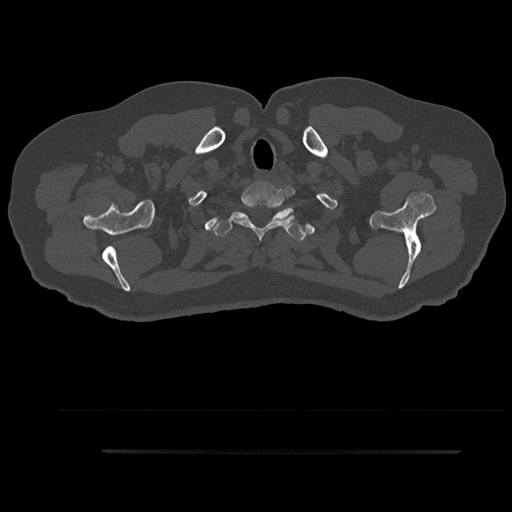
CT including the spine, one axial slice. Position 784 of 797 along the scan axis. Reconstruction kernel Br40s/3. 120 kVp. Bone window (W 1800 / L 400 HU). 0.5 mm slice thickness. 512 × 512 image matrix, field of view 432 × 432 mm. Male patient, age 63 years. Case-level facts recorded for this patient, not image findings: primary cancer: renal; vertebrae with lytic lesions (as recorded): T8.
Structures marked on this image (semi-automatically segmented with operator editing):
- T1 vertebra: box from (x=231, y=185) to (x=294, y=239) px
- T2 vertebra: (x=213, y=206)–(x=306, y=241)